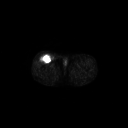
FDG PET of an extremity soft-tissue mass (from a PET/CT study), one axial slice; position 270 of 311 along the scan axis; 3.27 mm slice thickness; 128 × 128 image matrix. Patient: male, 56 years. From the clinical record (not read from this slice): histological type: pleiomorphic leiomyosarcoma; grade: intermediate; site of the primary tumour: right thigh.
Structures marked on this image (expert contour drawn on MRI and transferred to this co-registered scan by the dataset authors):
- gross tumour volume including surrounding oedema: bounding box [x1, y1, x2, y2] px = [39, 54, 51, 64]
- gross tumour volume (mass): [39, 54, 51, 63]